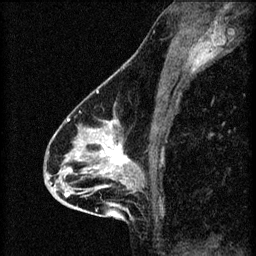
Breast MRI (dynamic contrast-enhanced), one sagittal slice. 3 images stored at this slice position (order not interpretable as contrast timing). 1.5 T. TE 4.2 ms, TR 8.2 ms. 2 mm slice thickness. 256 × 256 image matrix. Female patient, age 46 years.
Annotated regions visible in this slice (semi-automatic segmentation, software-assisted and operator-edited):
- analysis volume of interest (the breast-tissue region the enhancement analysis was run in; not a lesion): box from (x=55, y=114) to (x=145, y=209) px
- tumour enhancement mask (voxels above the 70 % enhancement threshold inside the analysis volume of interest): (x=64, y=120)–(x=135, y=197)